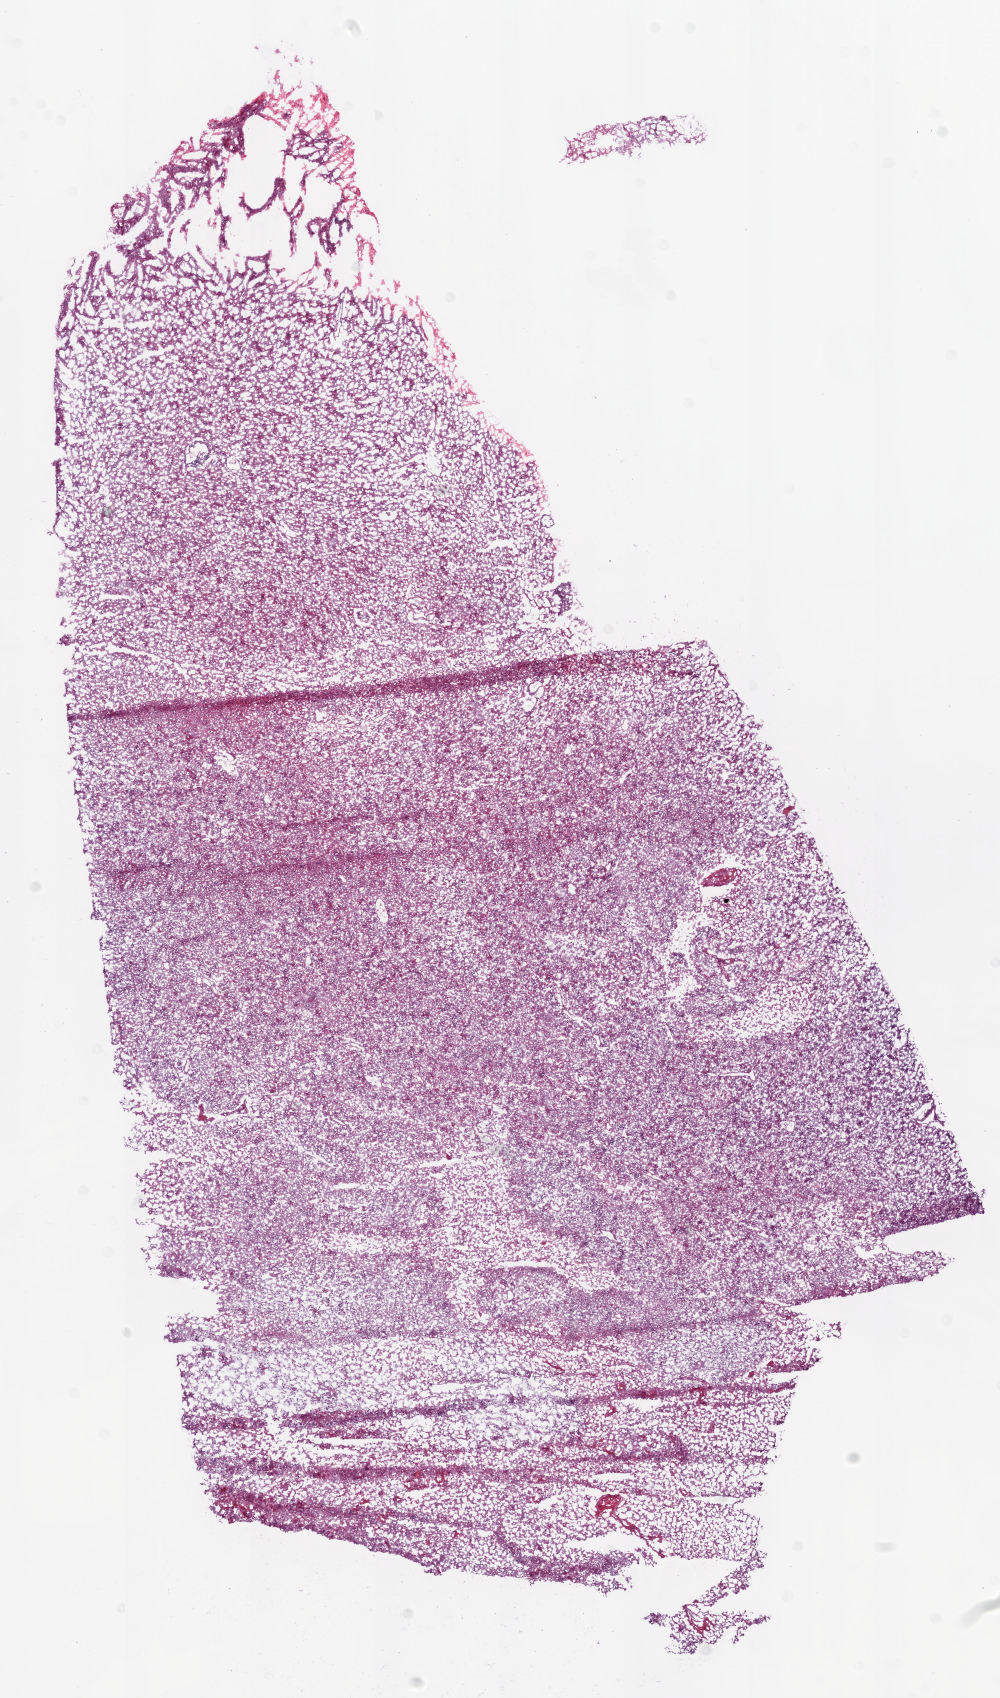
Whole-slide histology image, Hematoxylin and eosin (H&E) stained, whole scanned area (about 8.0 x 13.6 mm) shown as a low-resolution overview; frozen section from the top of the tissue portion; sample: primary tumour, brain. Patient: female, age at initial diagnosis 40 years. Composition of this section per pathologist review: tumour cells 80%, tumour nuclei 90%.
Histologic diagnosis: Glioblastoma.